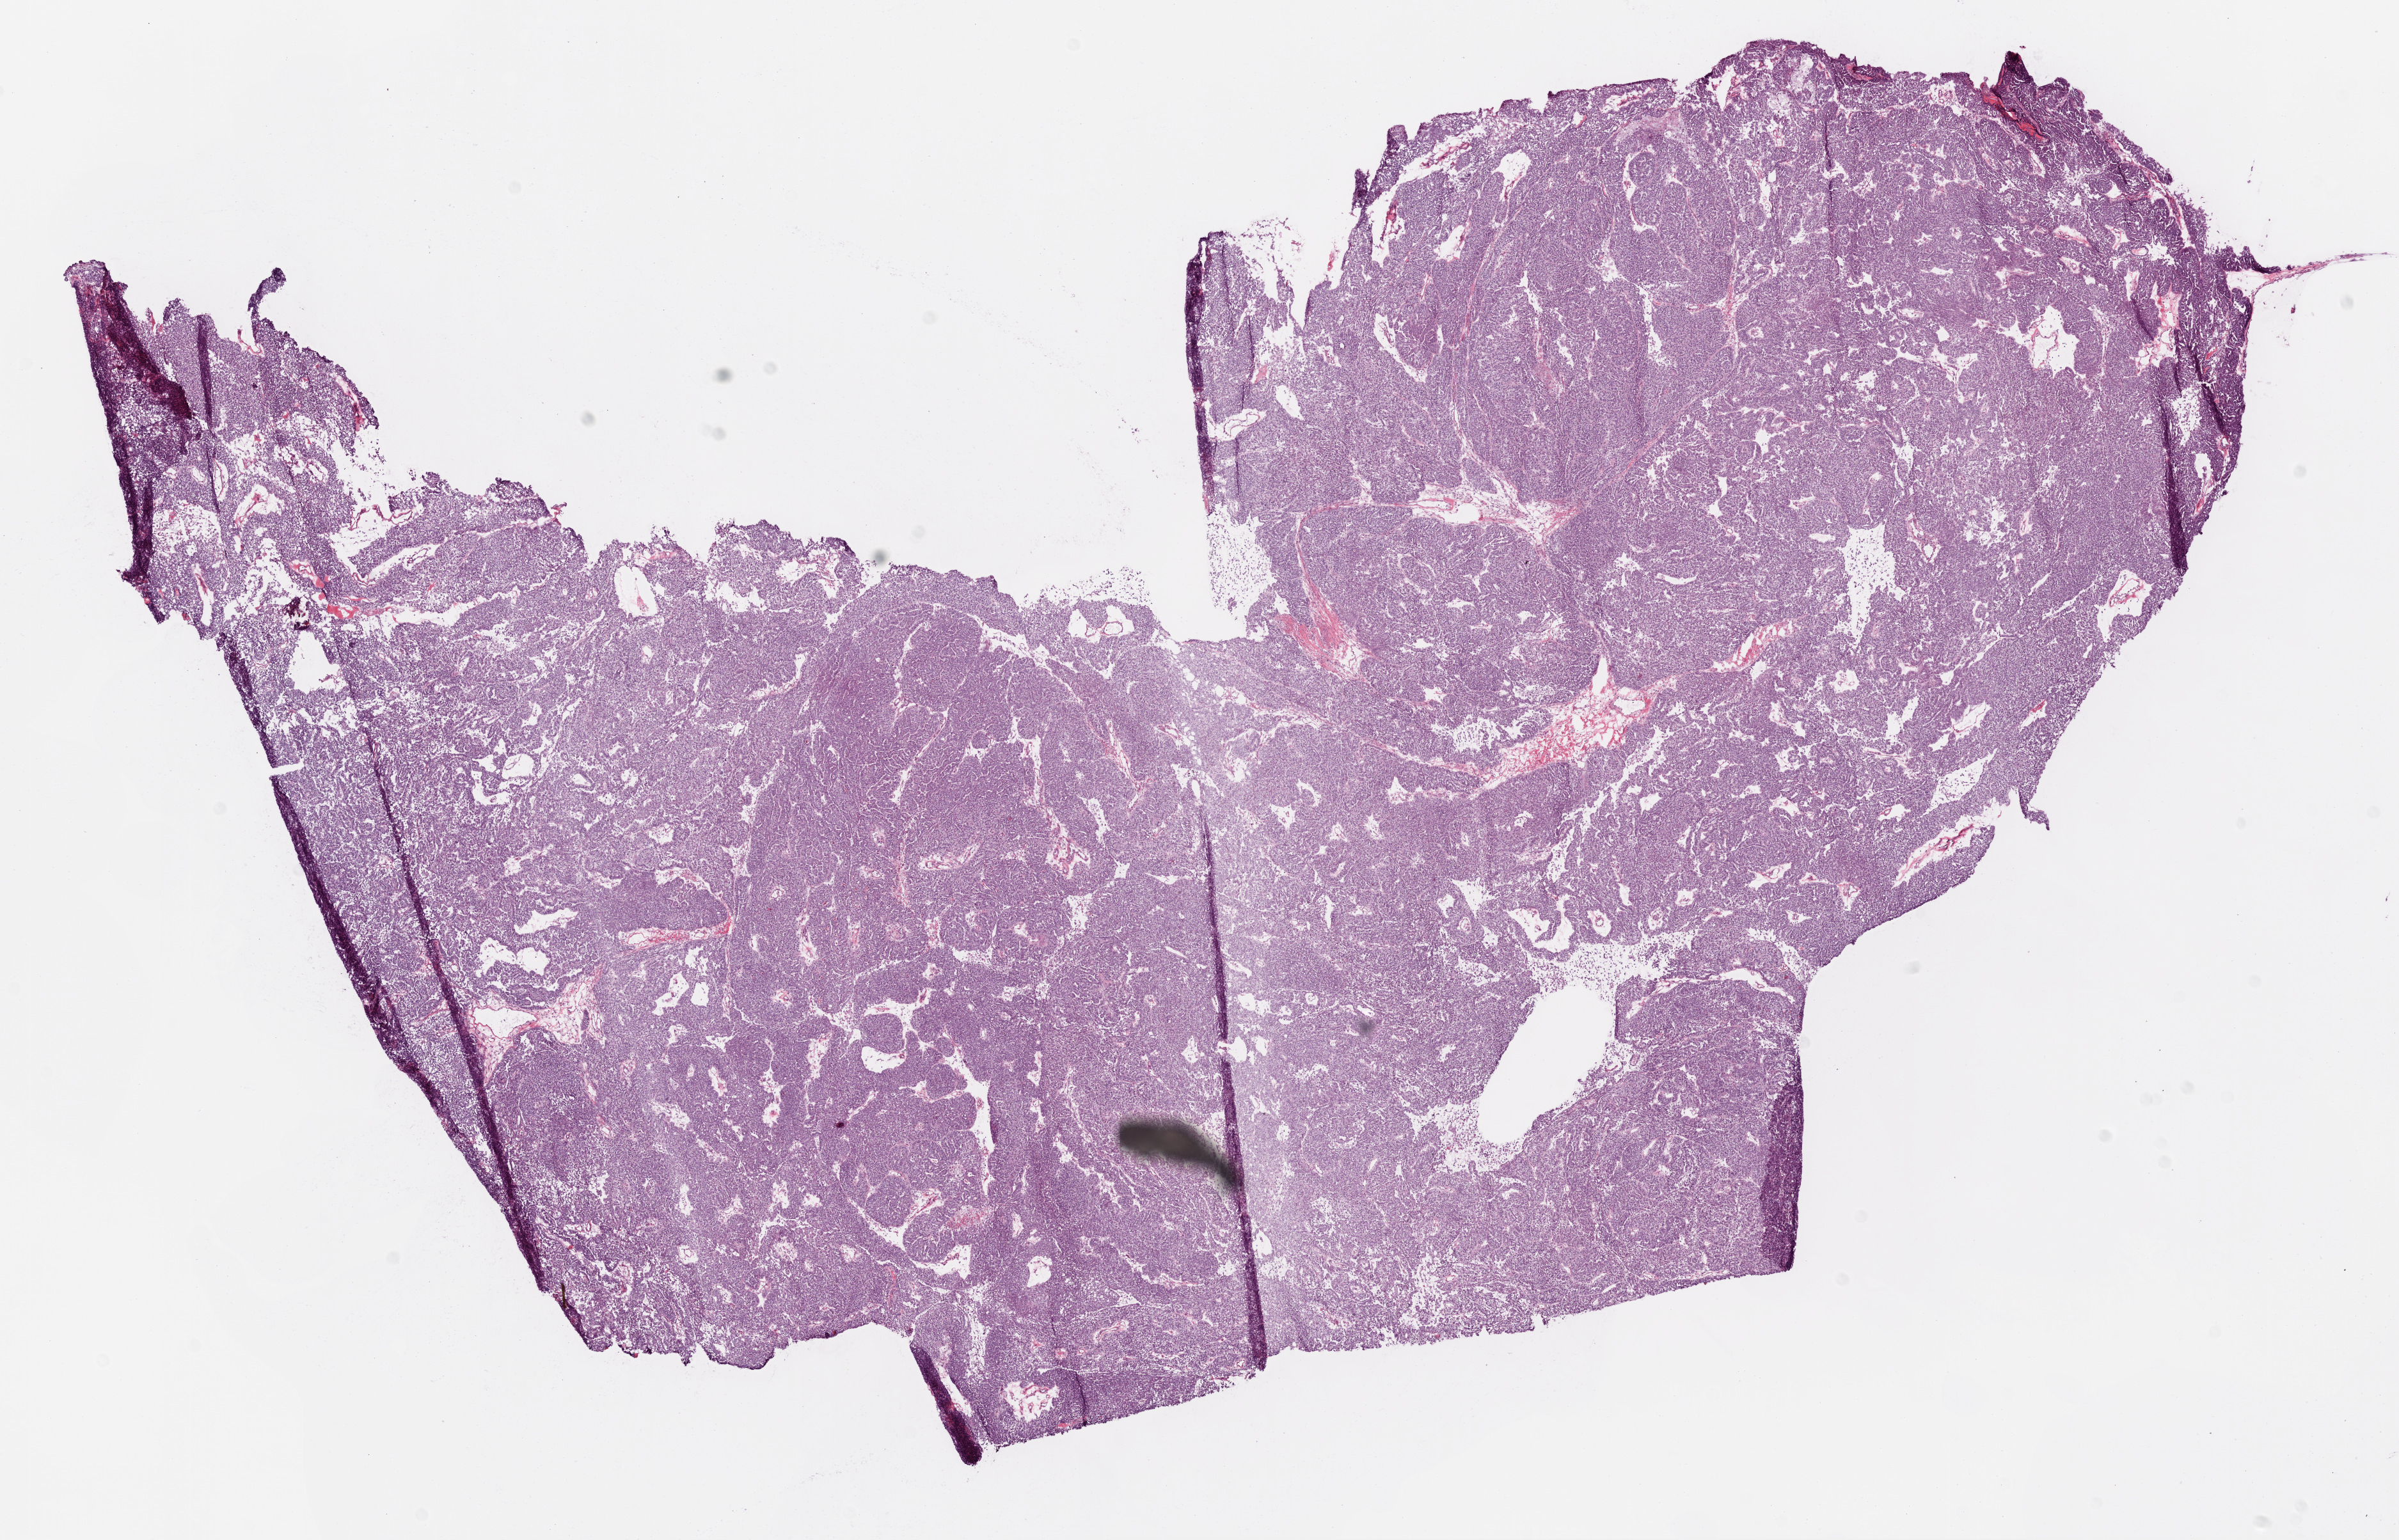
Digitized H&E tissue section (whole slide), low-resolution overview of the scanned area, about 15.0 x 9.7 mm. Frozen section from the top of the tissue portion. Primary tumour sample from the ovary. Patient: female, age at initial diagnosis 57 years. Histologic grade: G3 (poorly differentiated). Composition of this section per pathologist review: tumour cells 93%, tumour nuclei 95%, normal cells 0%, stromal cells 5%, necrosis 2%.
• laterality: bilateral
• histologic diagnosis: Serous cystadenocarcinoma, NOS
• FIGO stage: IIIC